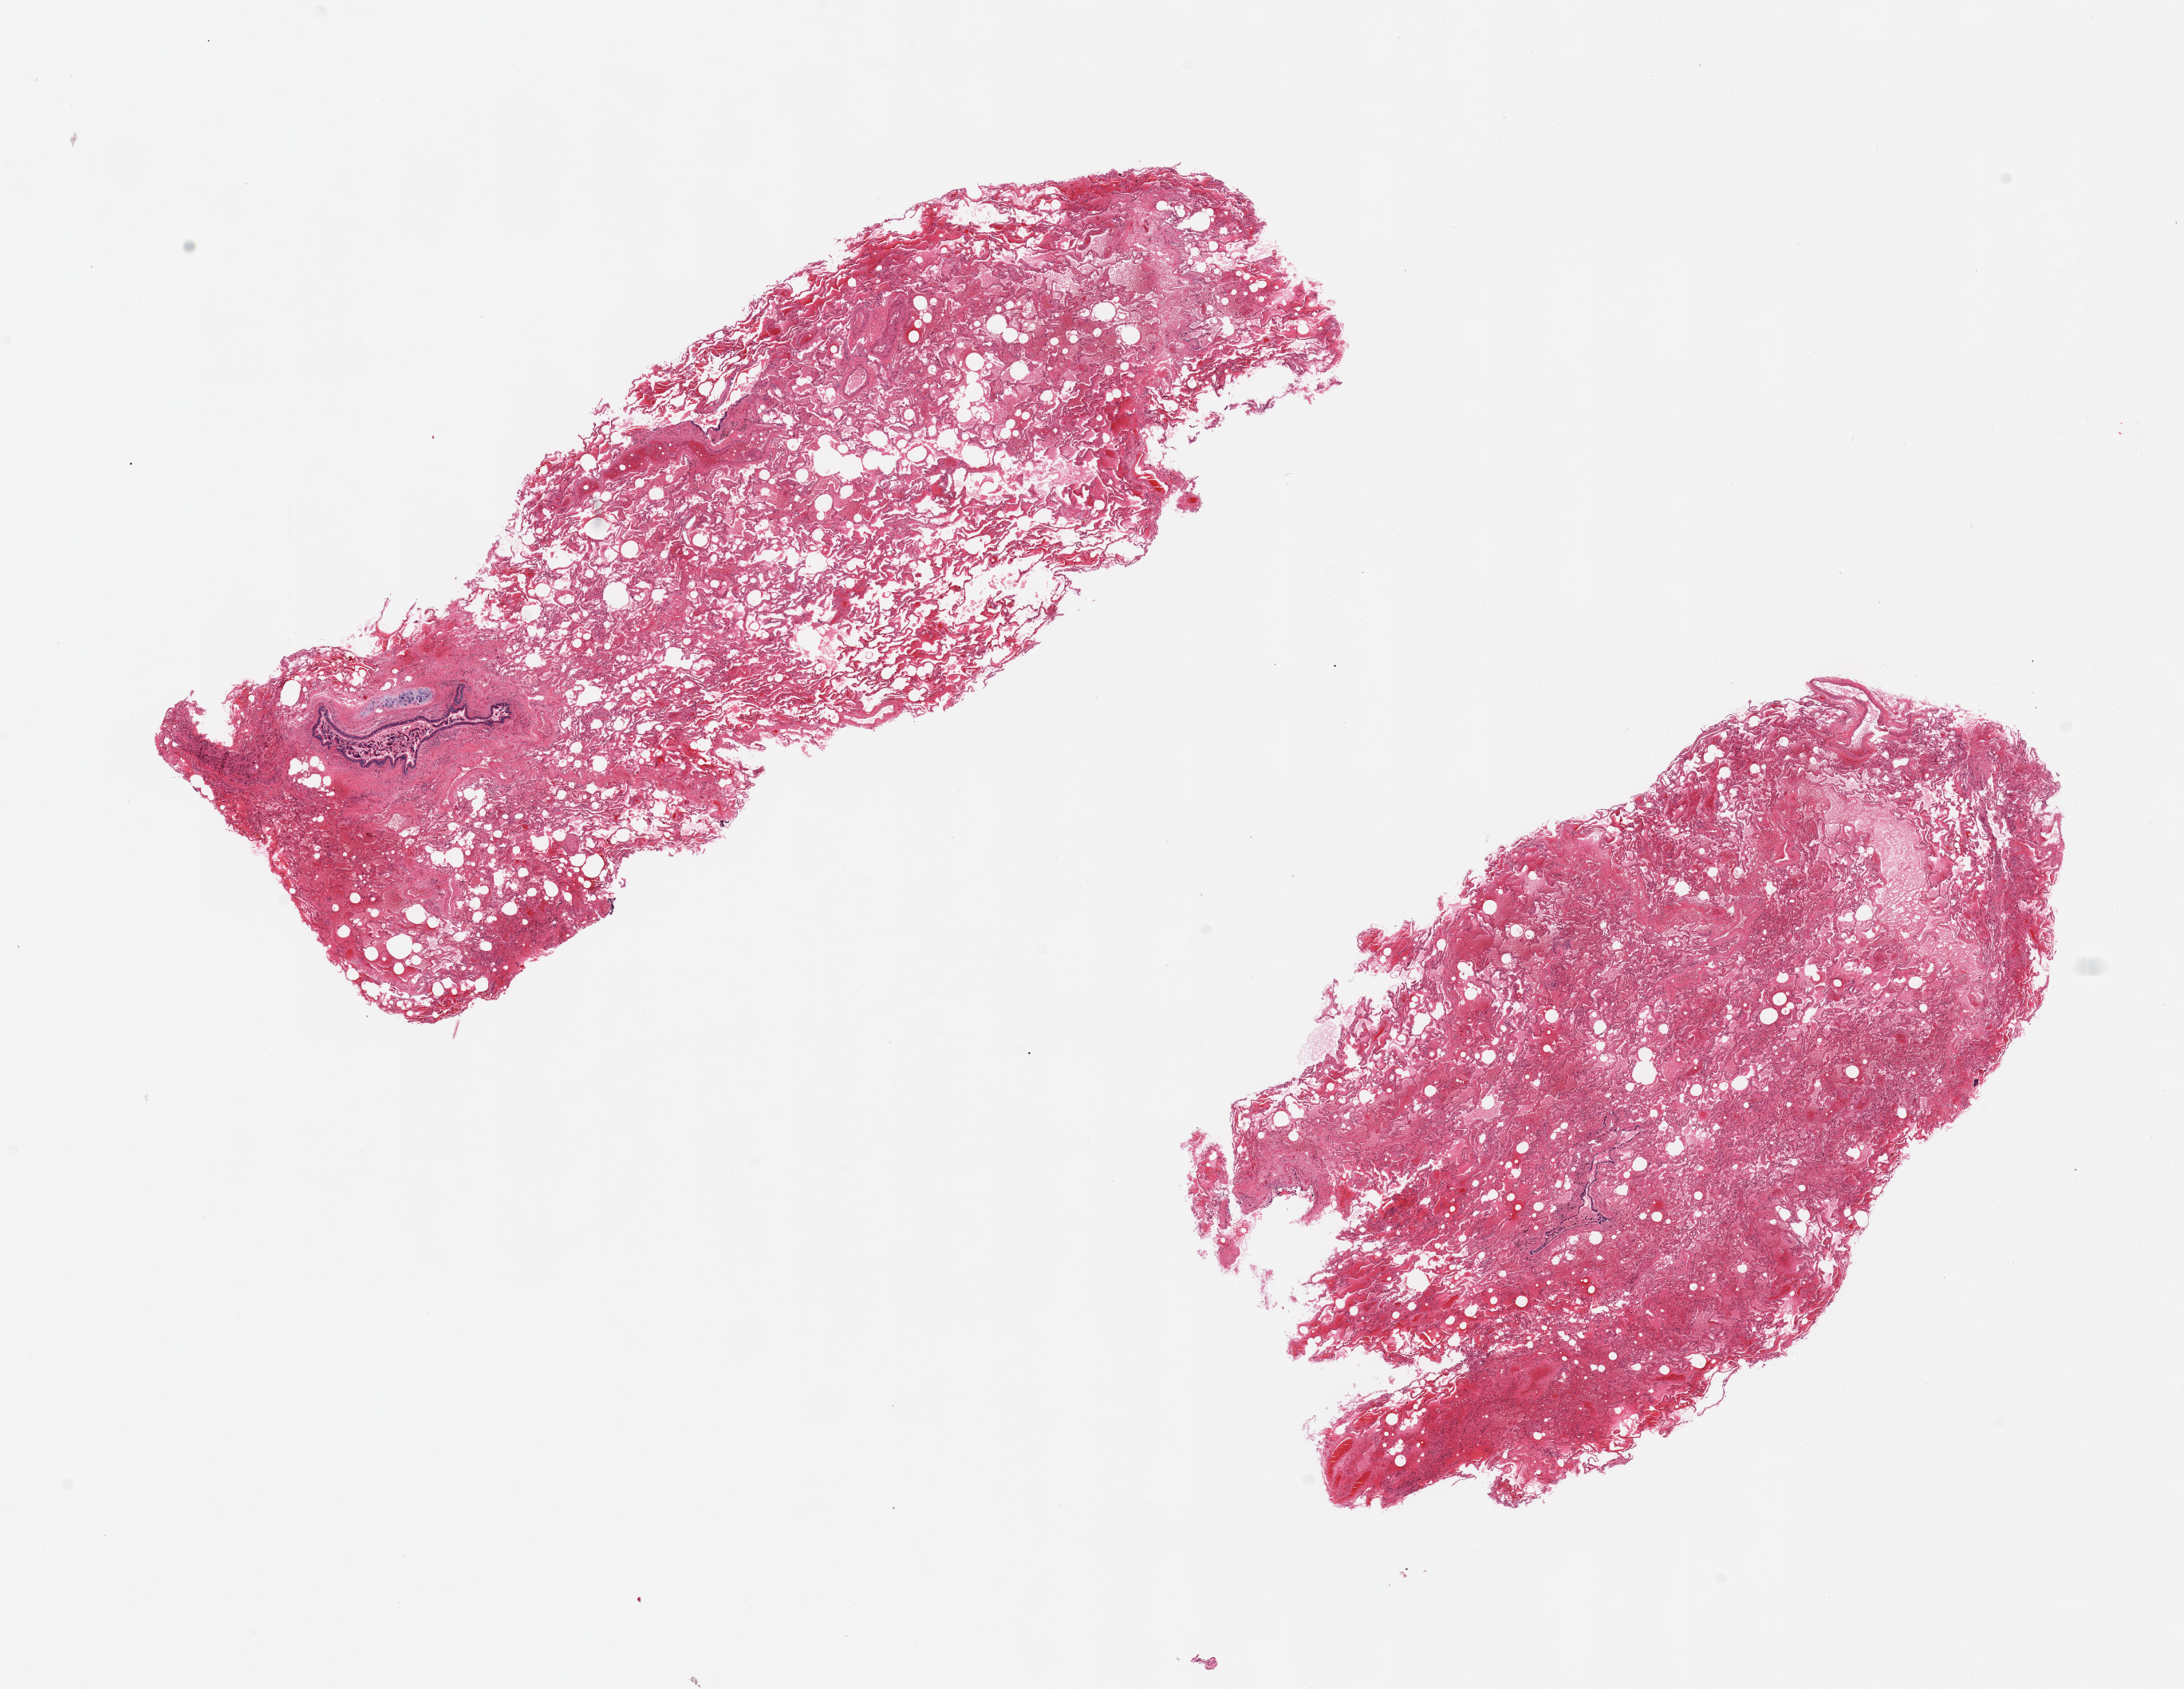
Digitized hematoxylin and eosin (H&E)-stained section, shown as a low-resolution overview of the whole scanned area (about 21.7 x 16.7 mm, acquisition: 20x scan). PAXgene-fixed paraffin-embedded (PFPE) section. Section of lung (target tissue). Tissue donor sample.
Reviewer comment on this tissue sample: 2 pieces, edema, hemorrhage, focus of cartilage.